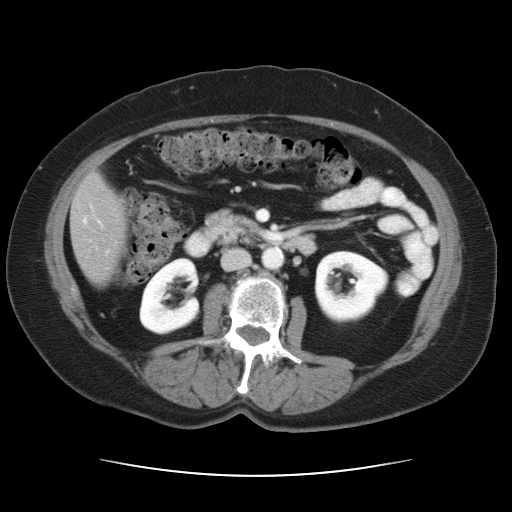
Contrast-enhanced abdominal CT, one axial slice; position 10 of 34 along the scan axis; 120 kVp; intravenous contrast given; soft-tissue window (W 400 / L 40 HU); 7.5 mm slice thickness; 512 × 512 image matrix. Female patient, age 65 years. Case-level facts recorded for this patient, not image findings: diagnosis: colorectal cancer liver metastases, imaged before liver resection; multiple liver metastases: yes; largest metastasis: 2.2 cm; disease in both lobes: no.
Annotated regions visible in this slice (manually delineated by an expert):
- liver: bounding box (x1, y1, x2, y2) in pixels: (73, 176, 124, 279)
- planned liver remnant (the part of the liver to remain after resection): (73, 176, 124, 279)